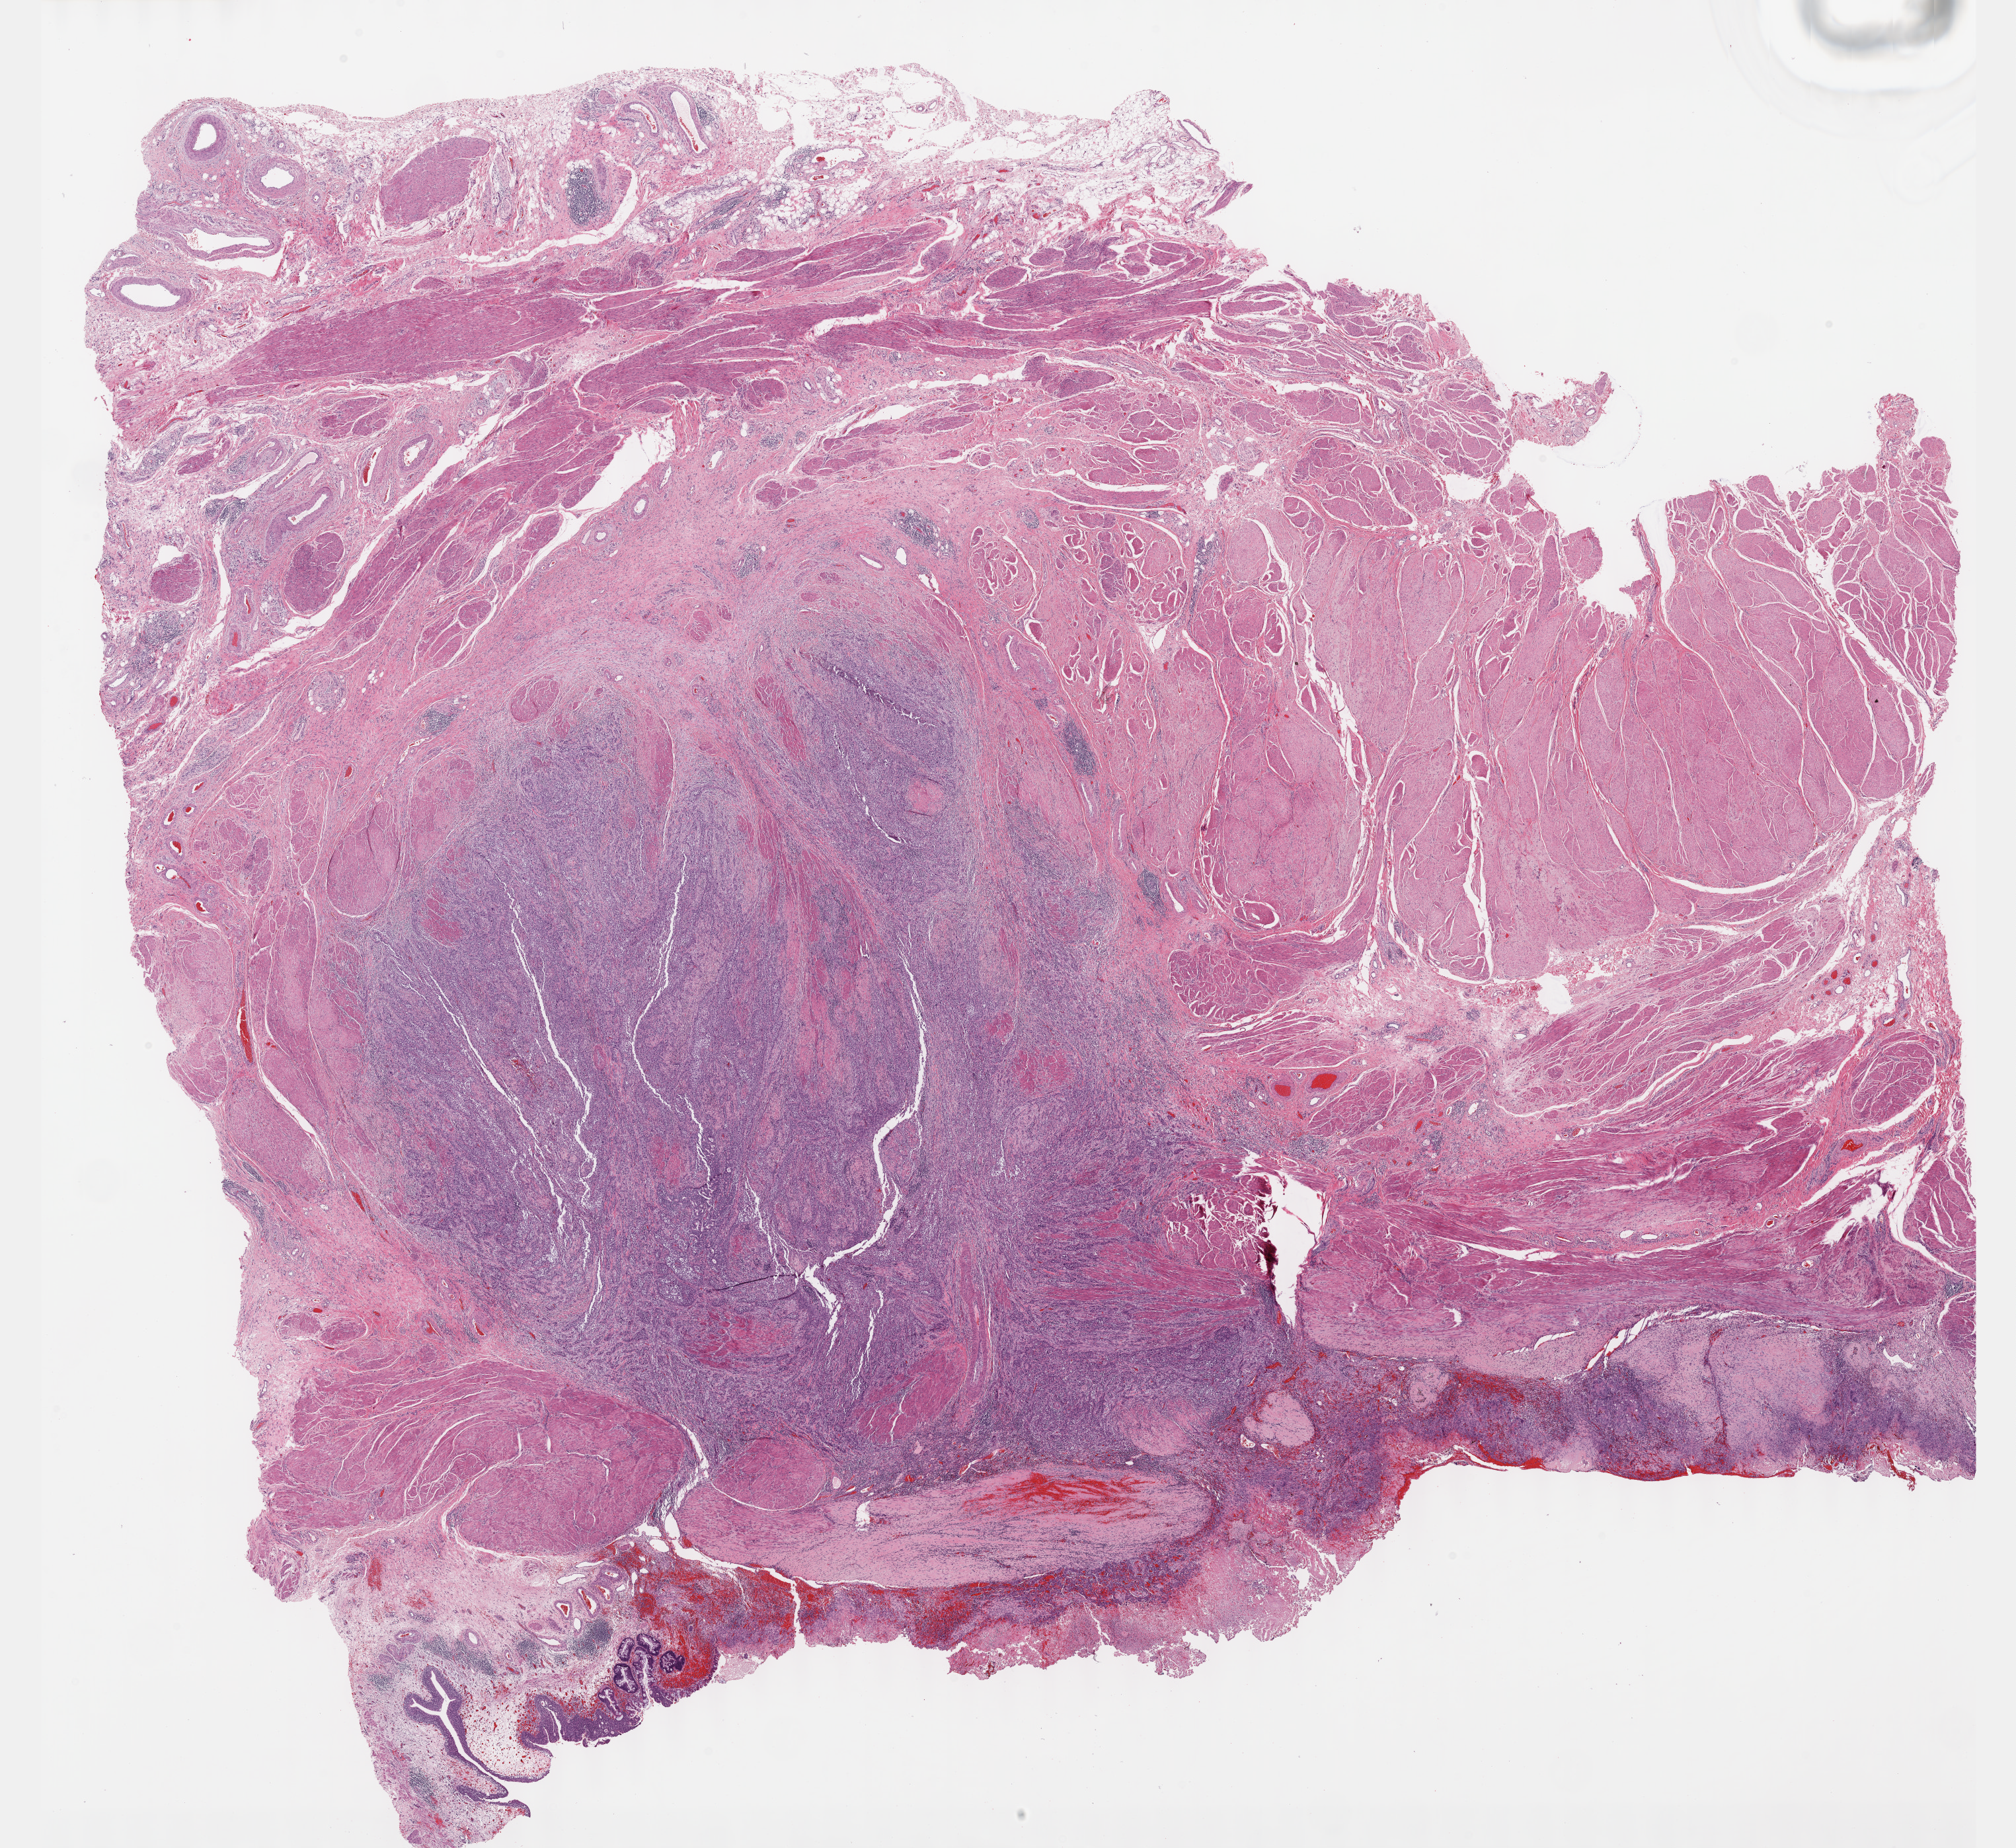
Digitized Hematoxylin and eosin (H&E) stained tissue section (whole slide), a low-resolution overview of the entire scanned area, about 24.6 x 22.6 mm; FFPE section; sample: primary tumour, bladder. Male patient; age at initial diagnosis 66 years. Histologic grade: high grade.
Lymph nodes positive (case pathology): 0 of 19 examined. Pathologic diagnosis: Transitional cell carcinoma (anterior wall of bladder). AJCC pathologic stage: II (7th edition). TNM: T2b N0 MX.